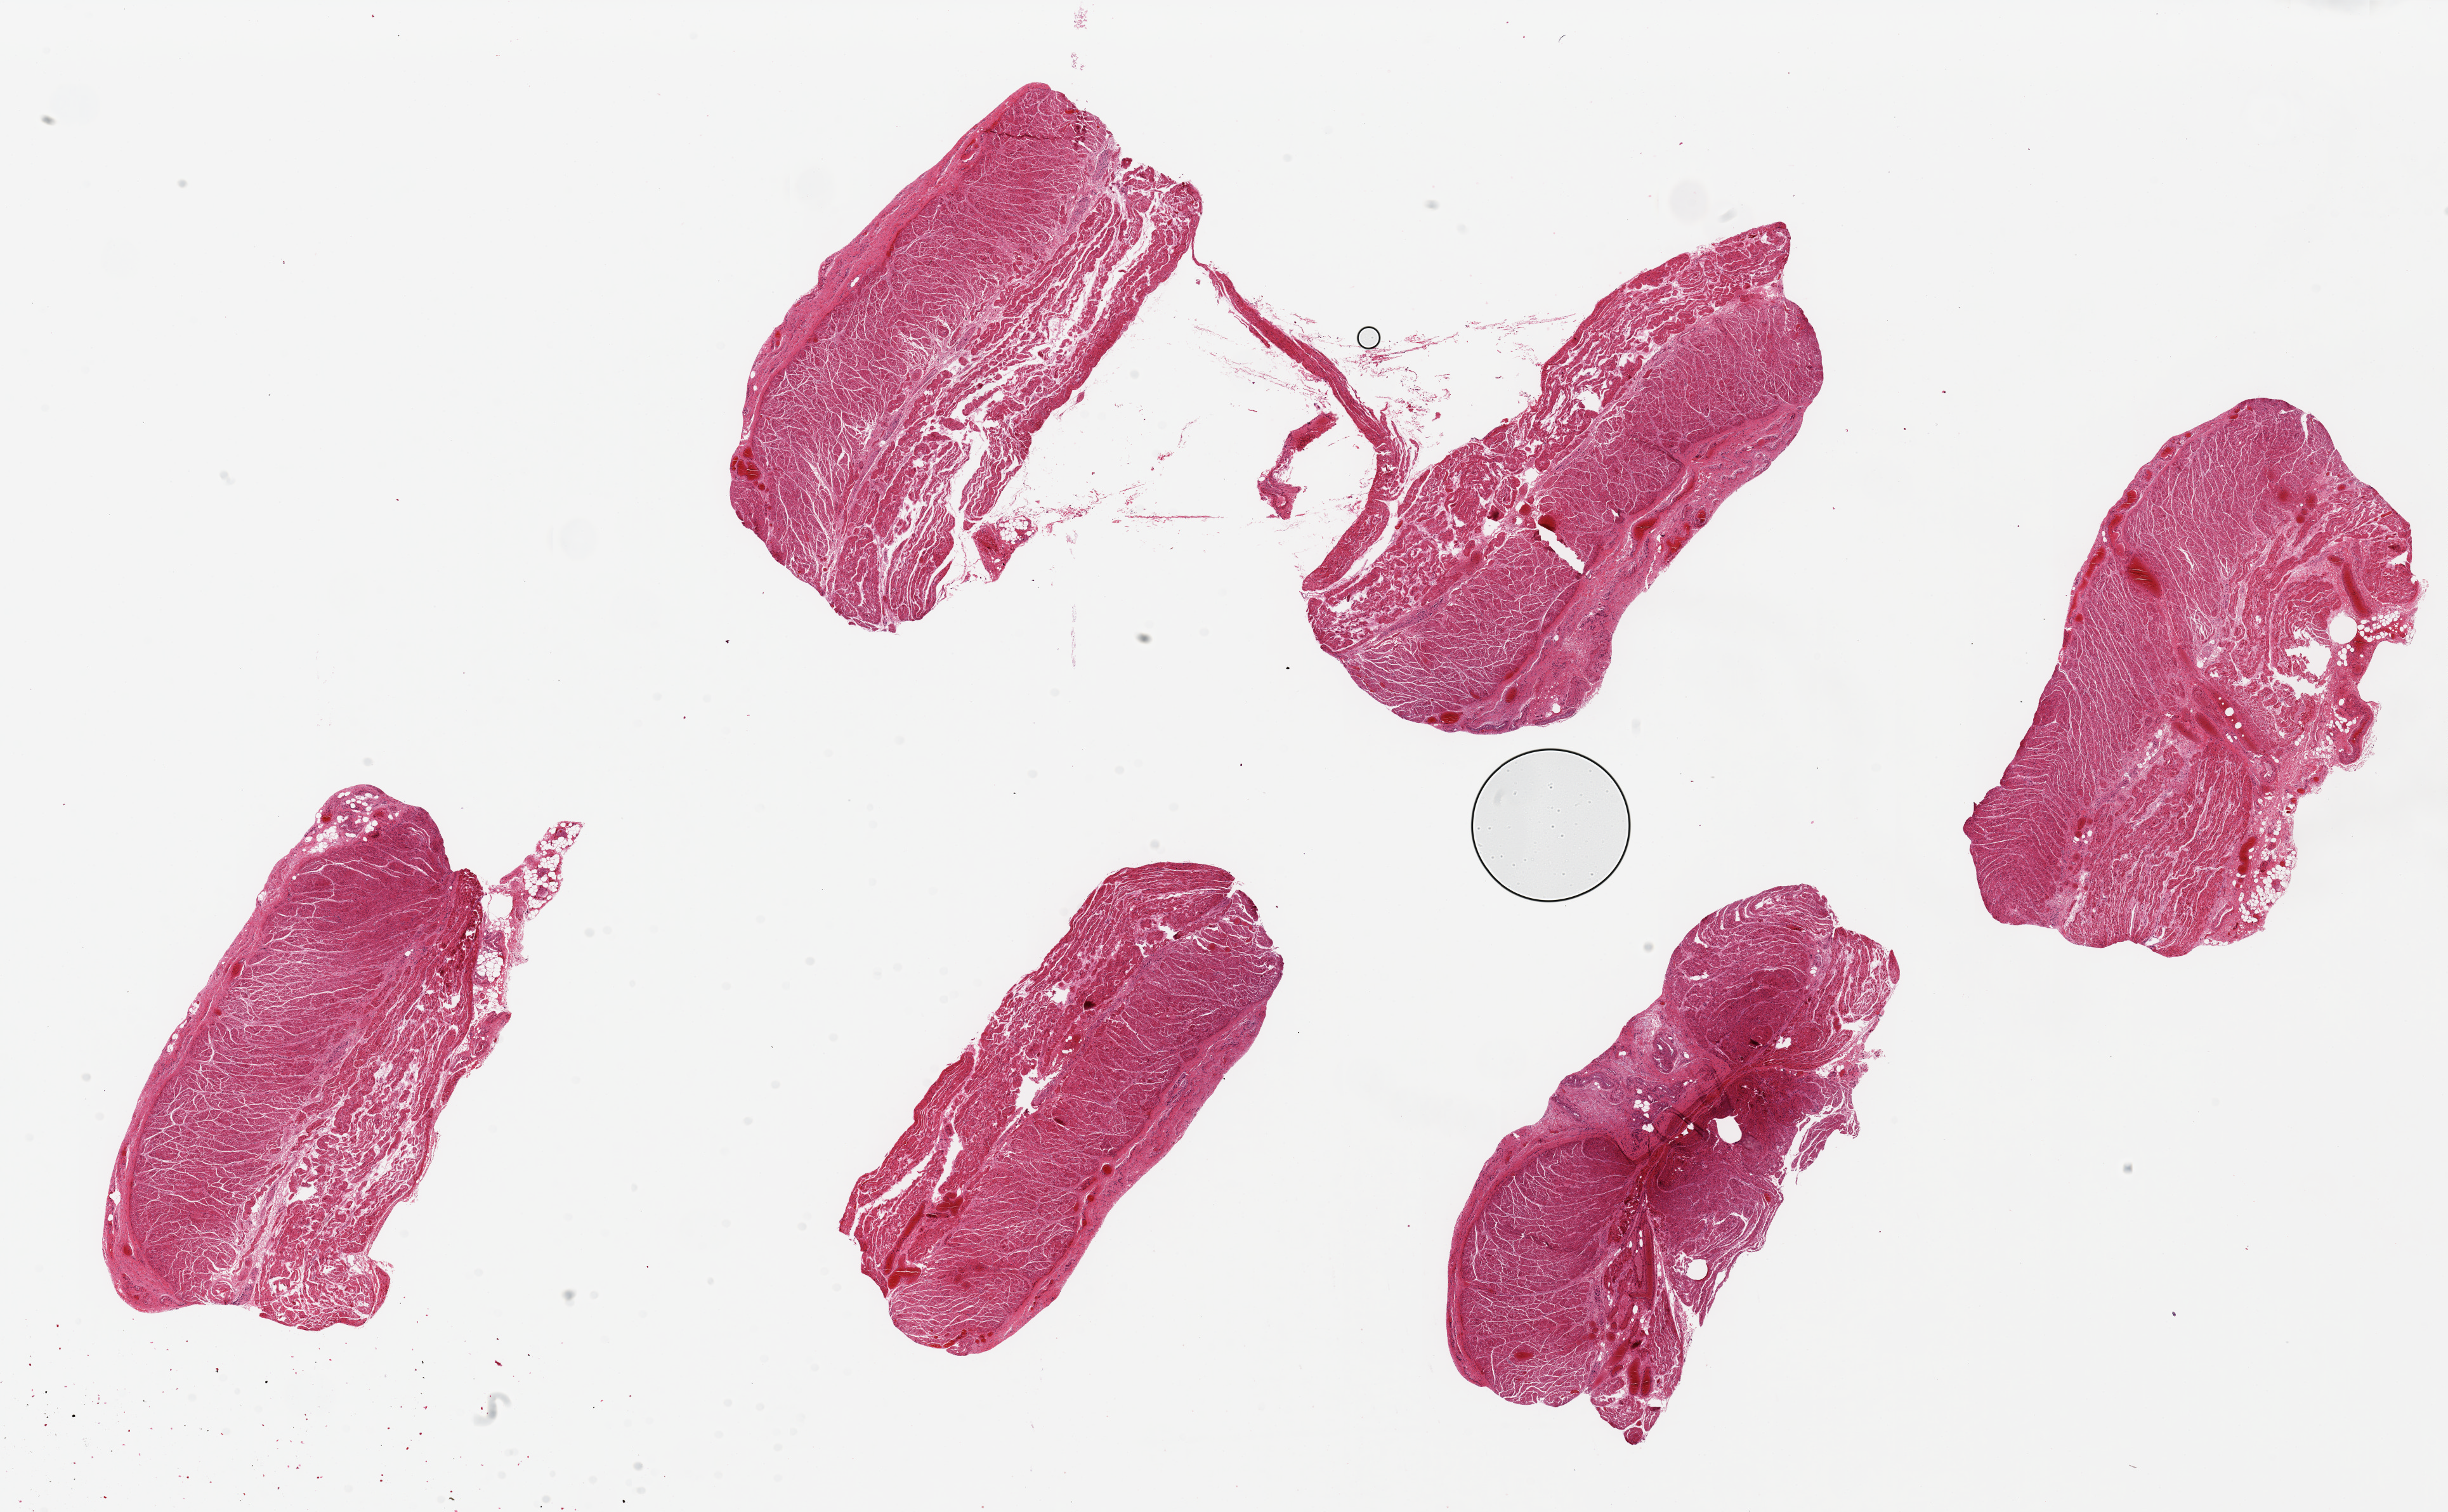
Hematoxylin and eosin (H&E) whole-slide image, brightfield — whole scanned area (about 30.5 x 18.9 mm) shown as a low-resolution overview. PAXgene-fixed paraffin-embedded (PFPE) section. Section of gastroesophageal junction (target tissue). Donor tissue sample. Male donor.
• pathologist's review note for this sample: 6 pieces * x 2.5mm, all muscularis